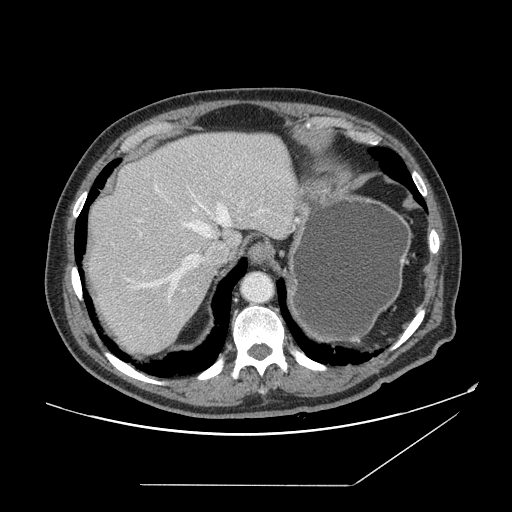
Contrast-enhanced abdominal CT, one axial slice. Position 125 of 166 along the scan axis. Intravenous contrast given. Soft-tissue window (W 400 / L 40 HU). 2.5 mm slice thickness. 512 × 512 image matrix, field of view 416 × 416 mm. Male patient, age 80 years. From the clinical record (not read from this slice): diagnosis: colorectal cancer liver metastases, imaged before liver resection; multiple liver metastases: no; largest metastasis: 2.2 cm; disease in both lobes: no.
Outlined on this slice (outlined manually by an expert reader):
- hepatic veins: box from (x=134, y=187) to (x=243, y=300) px
- liver: (x=87, y=133)–(x=295, y=354)
- planned liver remnant (the part of the liver to remain after resection): (x=88, y=133)–(x=295, y=256)
- portal vein (with intrahepatic branches): (x=141, y=209)–(x=196, y=272)